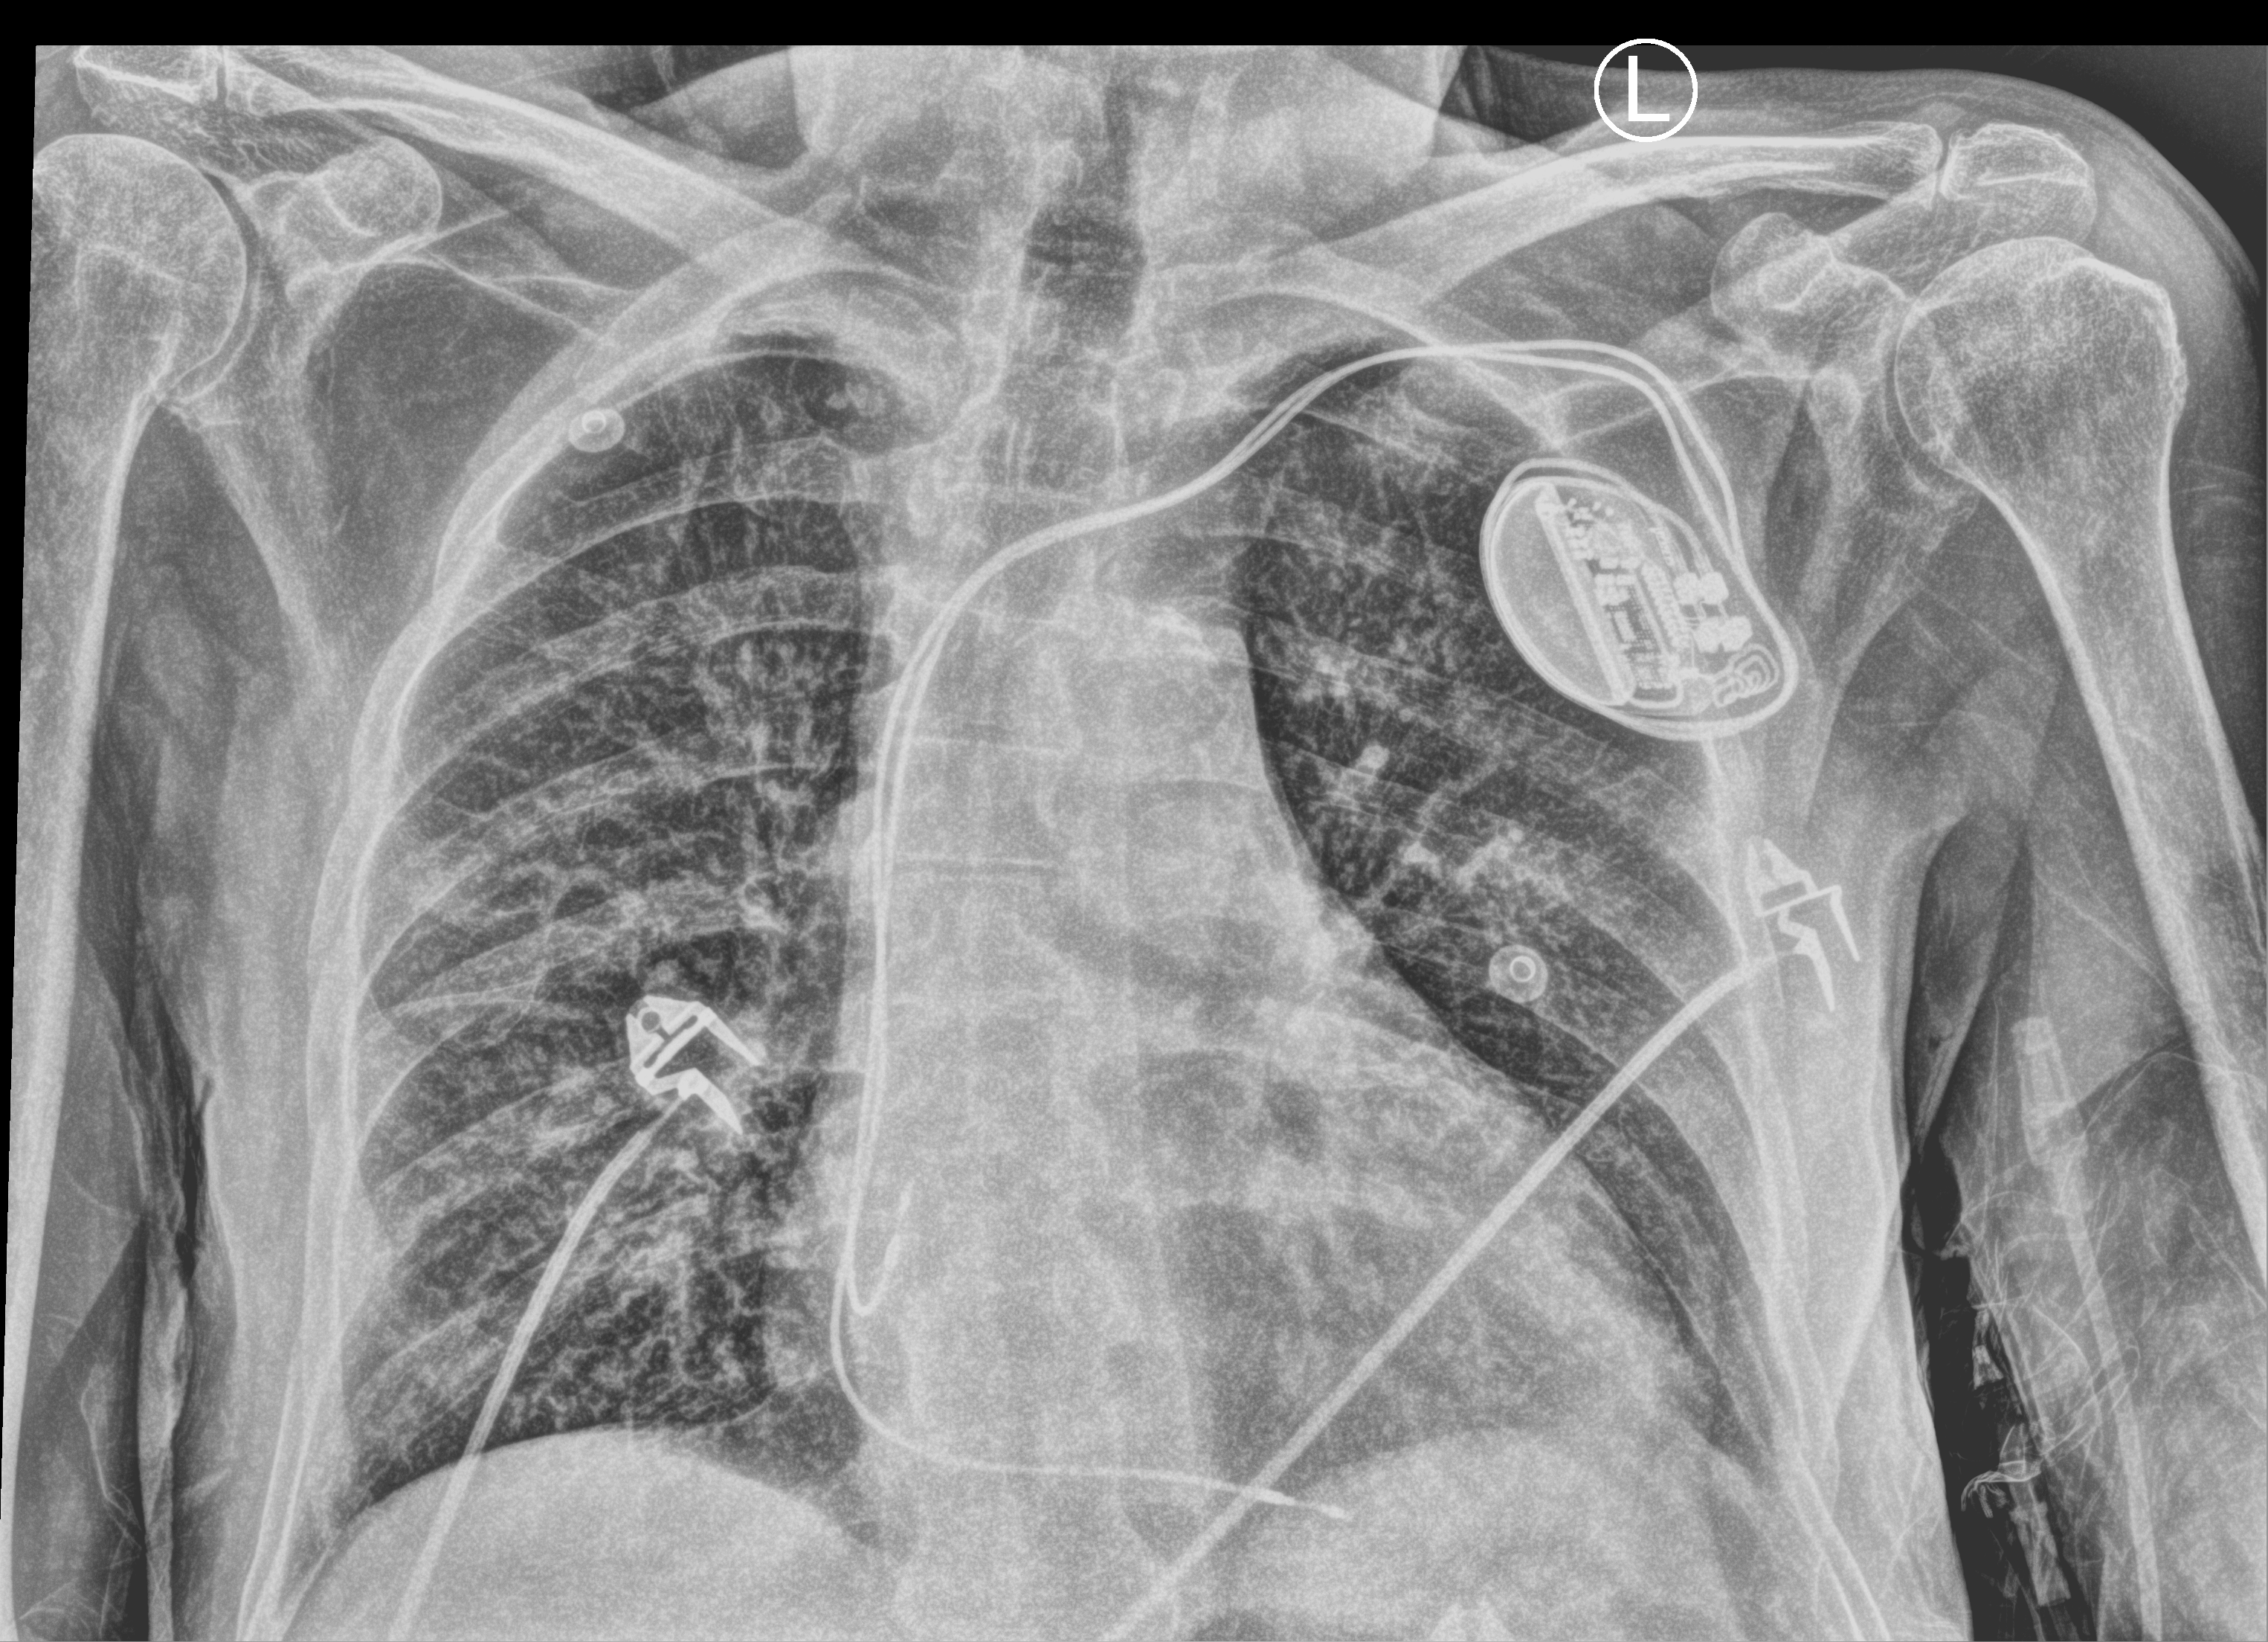
Chest X-ray (portable), anteroposterior (AP) projection. Male patient hospitalised with COVID-19, age 75–90 years.
From the hospital-stay record, not from the radiograph (when in the stay this image was taken is not recorded): mechanically ventilated during this hospital stay: no; length of hospital stay: 5 days; hypertension (admission record): yes.